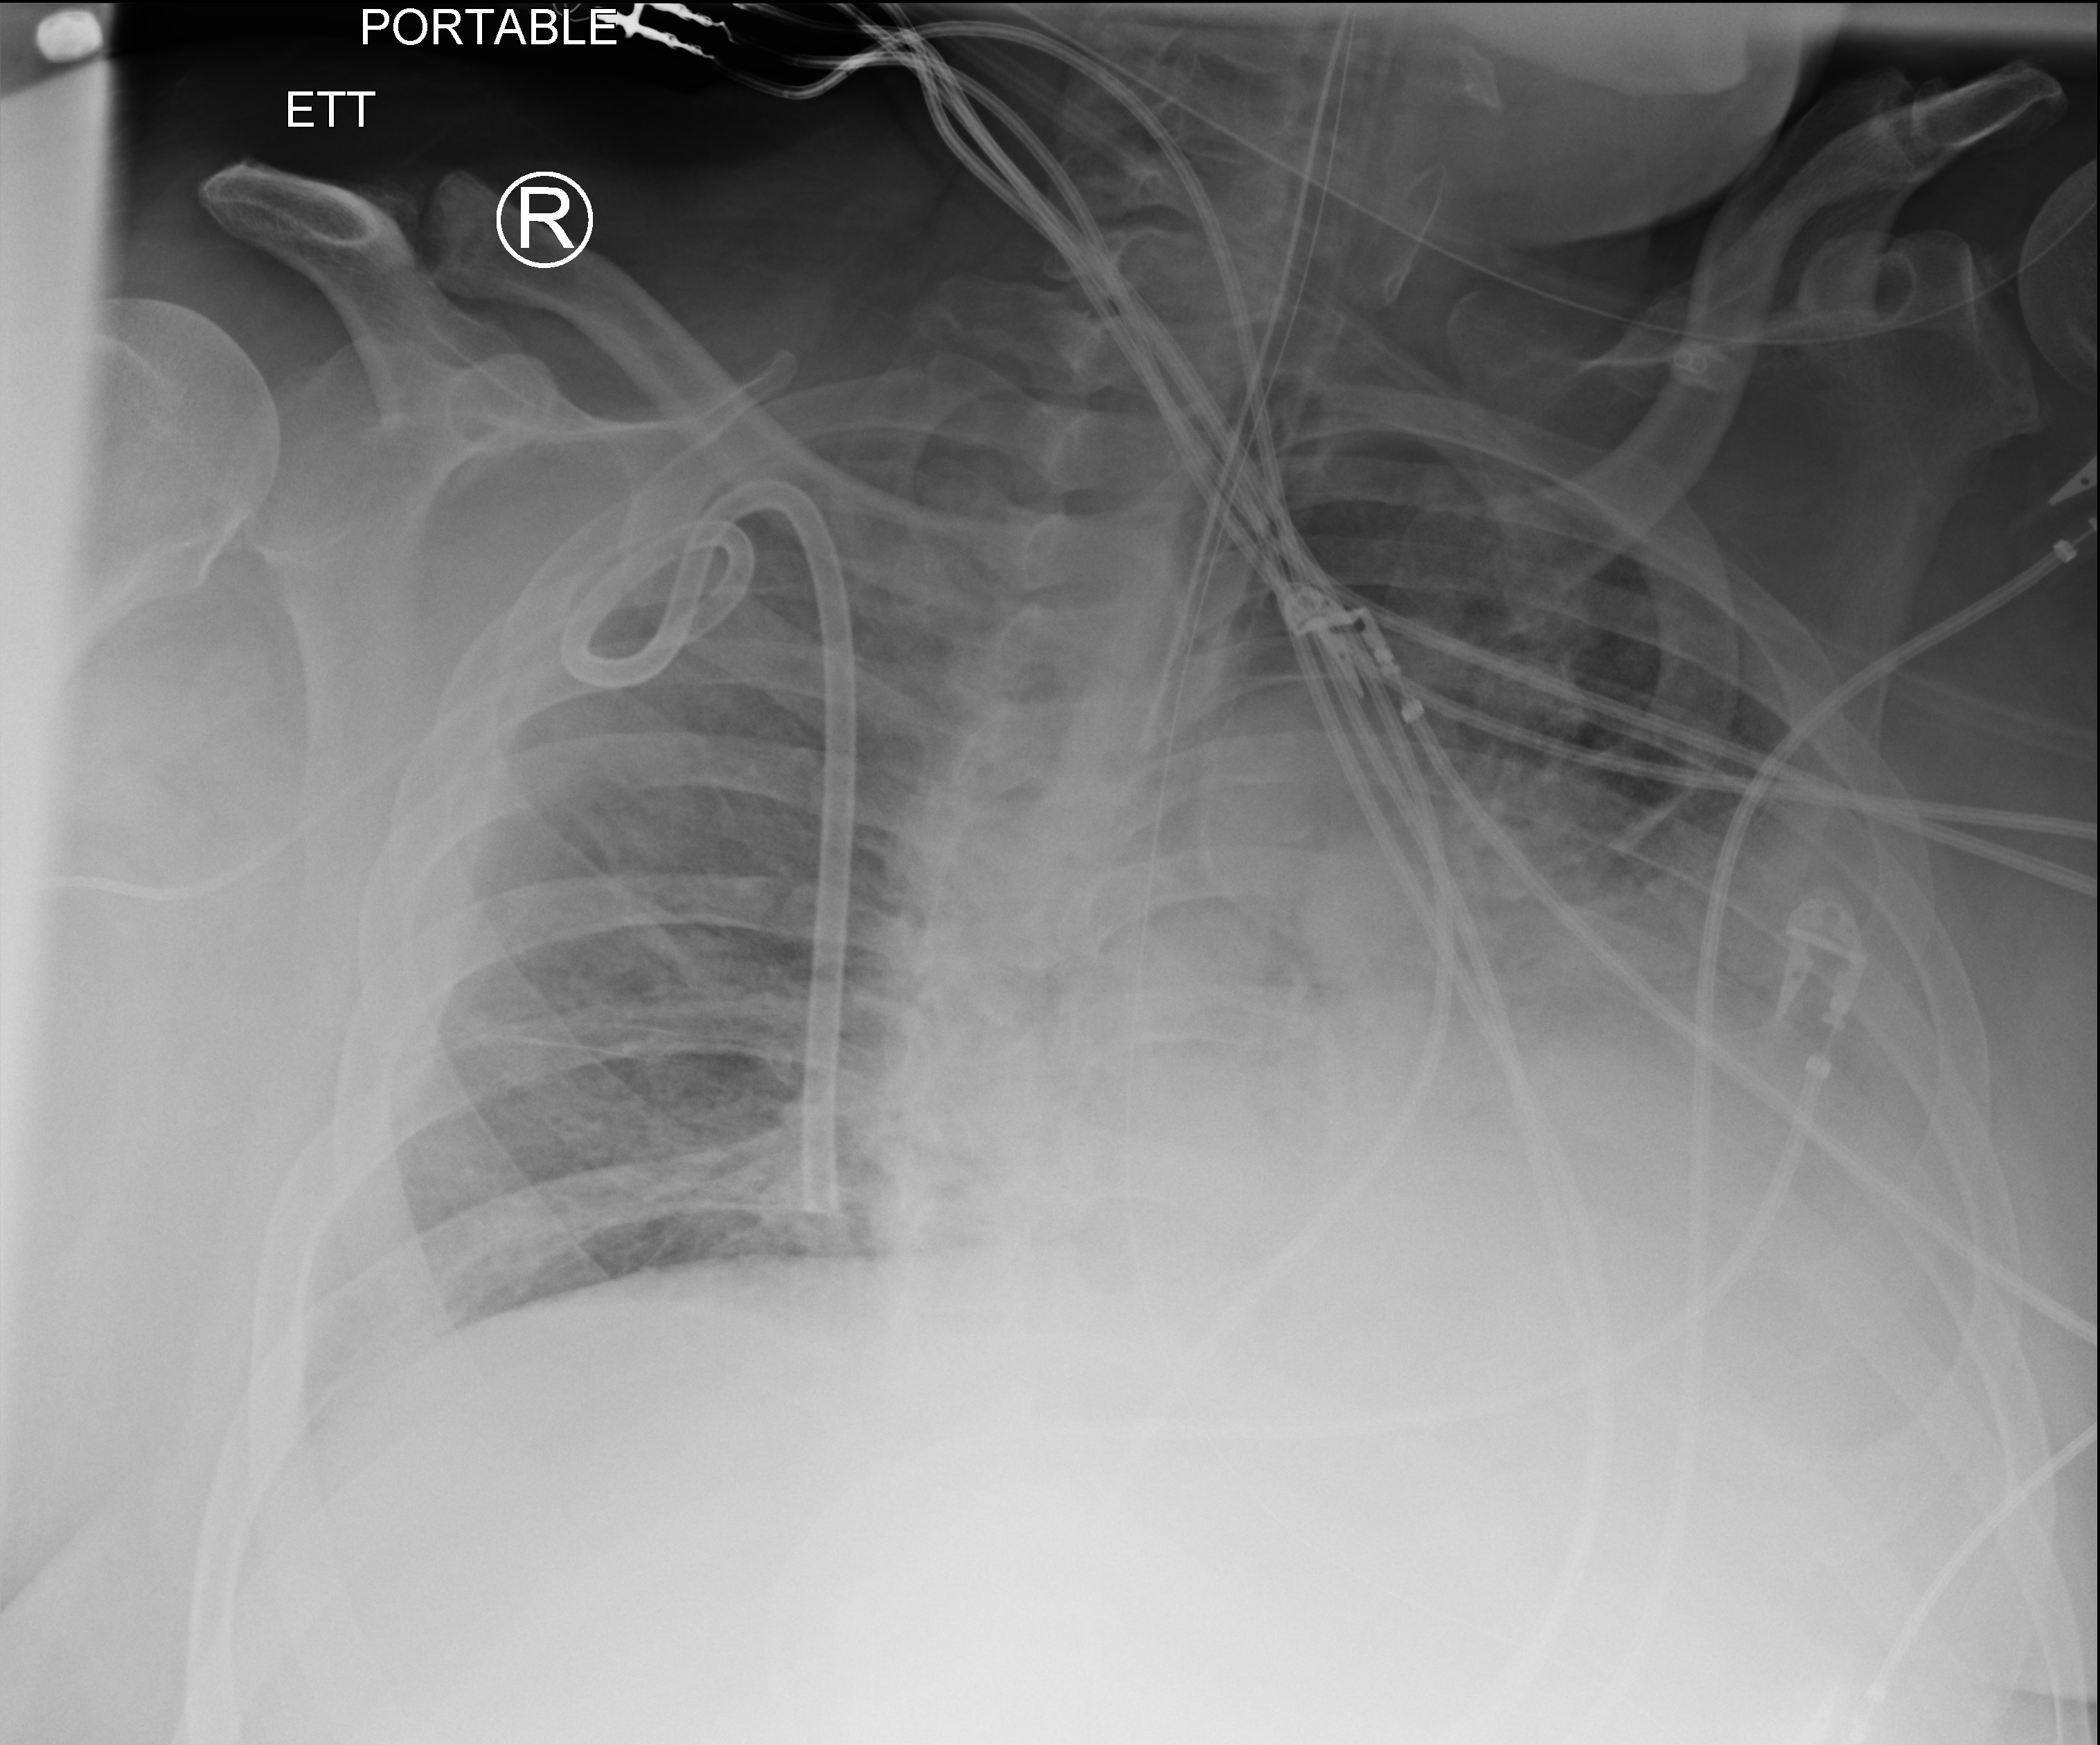
Chest X-ray (portable). Patient hospitalised with COVID-19; male, aged 60–74 years.
From the hospital-stay record, not from the radiograph (when in the stay this image was taken is not recorded): hypertension (admission record): yes.